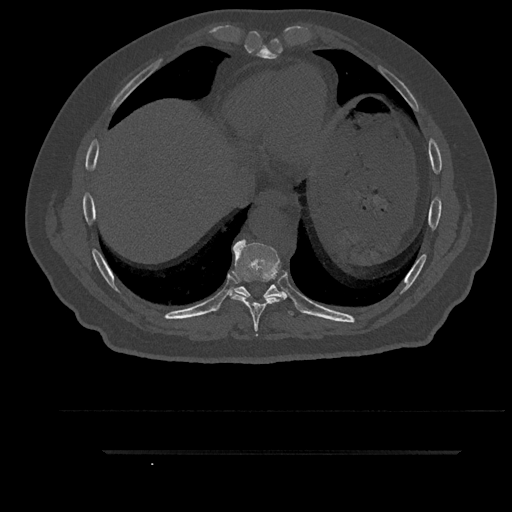
CT including the spine, one axial slice; slice 452 of 797 in the series (ordered by position); bone window (W 1800 / L 400 HU); 0.5 mm slice thickness; 512 × 512 image matrix. Patient: male, 63 years. Case-level facts recorded for this patient, not image findings: primary cancer: renal.
Annotated regions visible in this slice (semi-automatic segmentation, software-assisted and operator-edited):
- T10 vertebra: bounding box (x1, y1, x2, y2) in pixels: (281, 291, 284, 298)
- T8 vertebra: (230, 239, 286, 336)
- T9 vertebra: (231, 284, 294, 315)